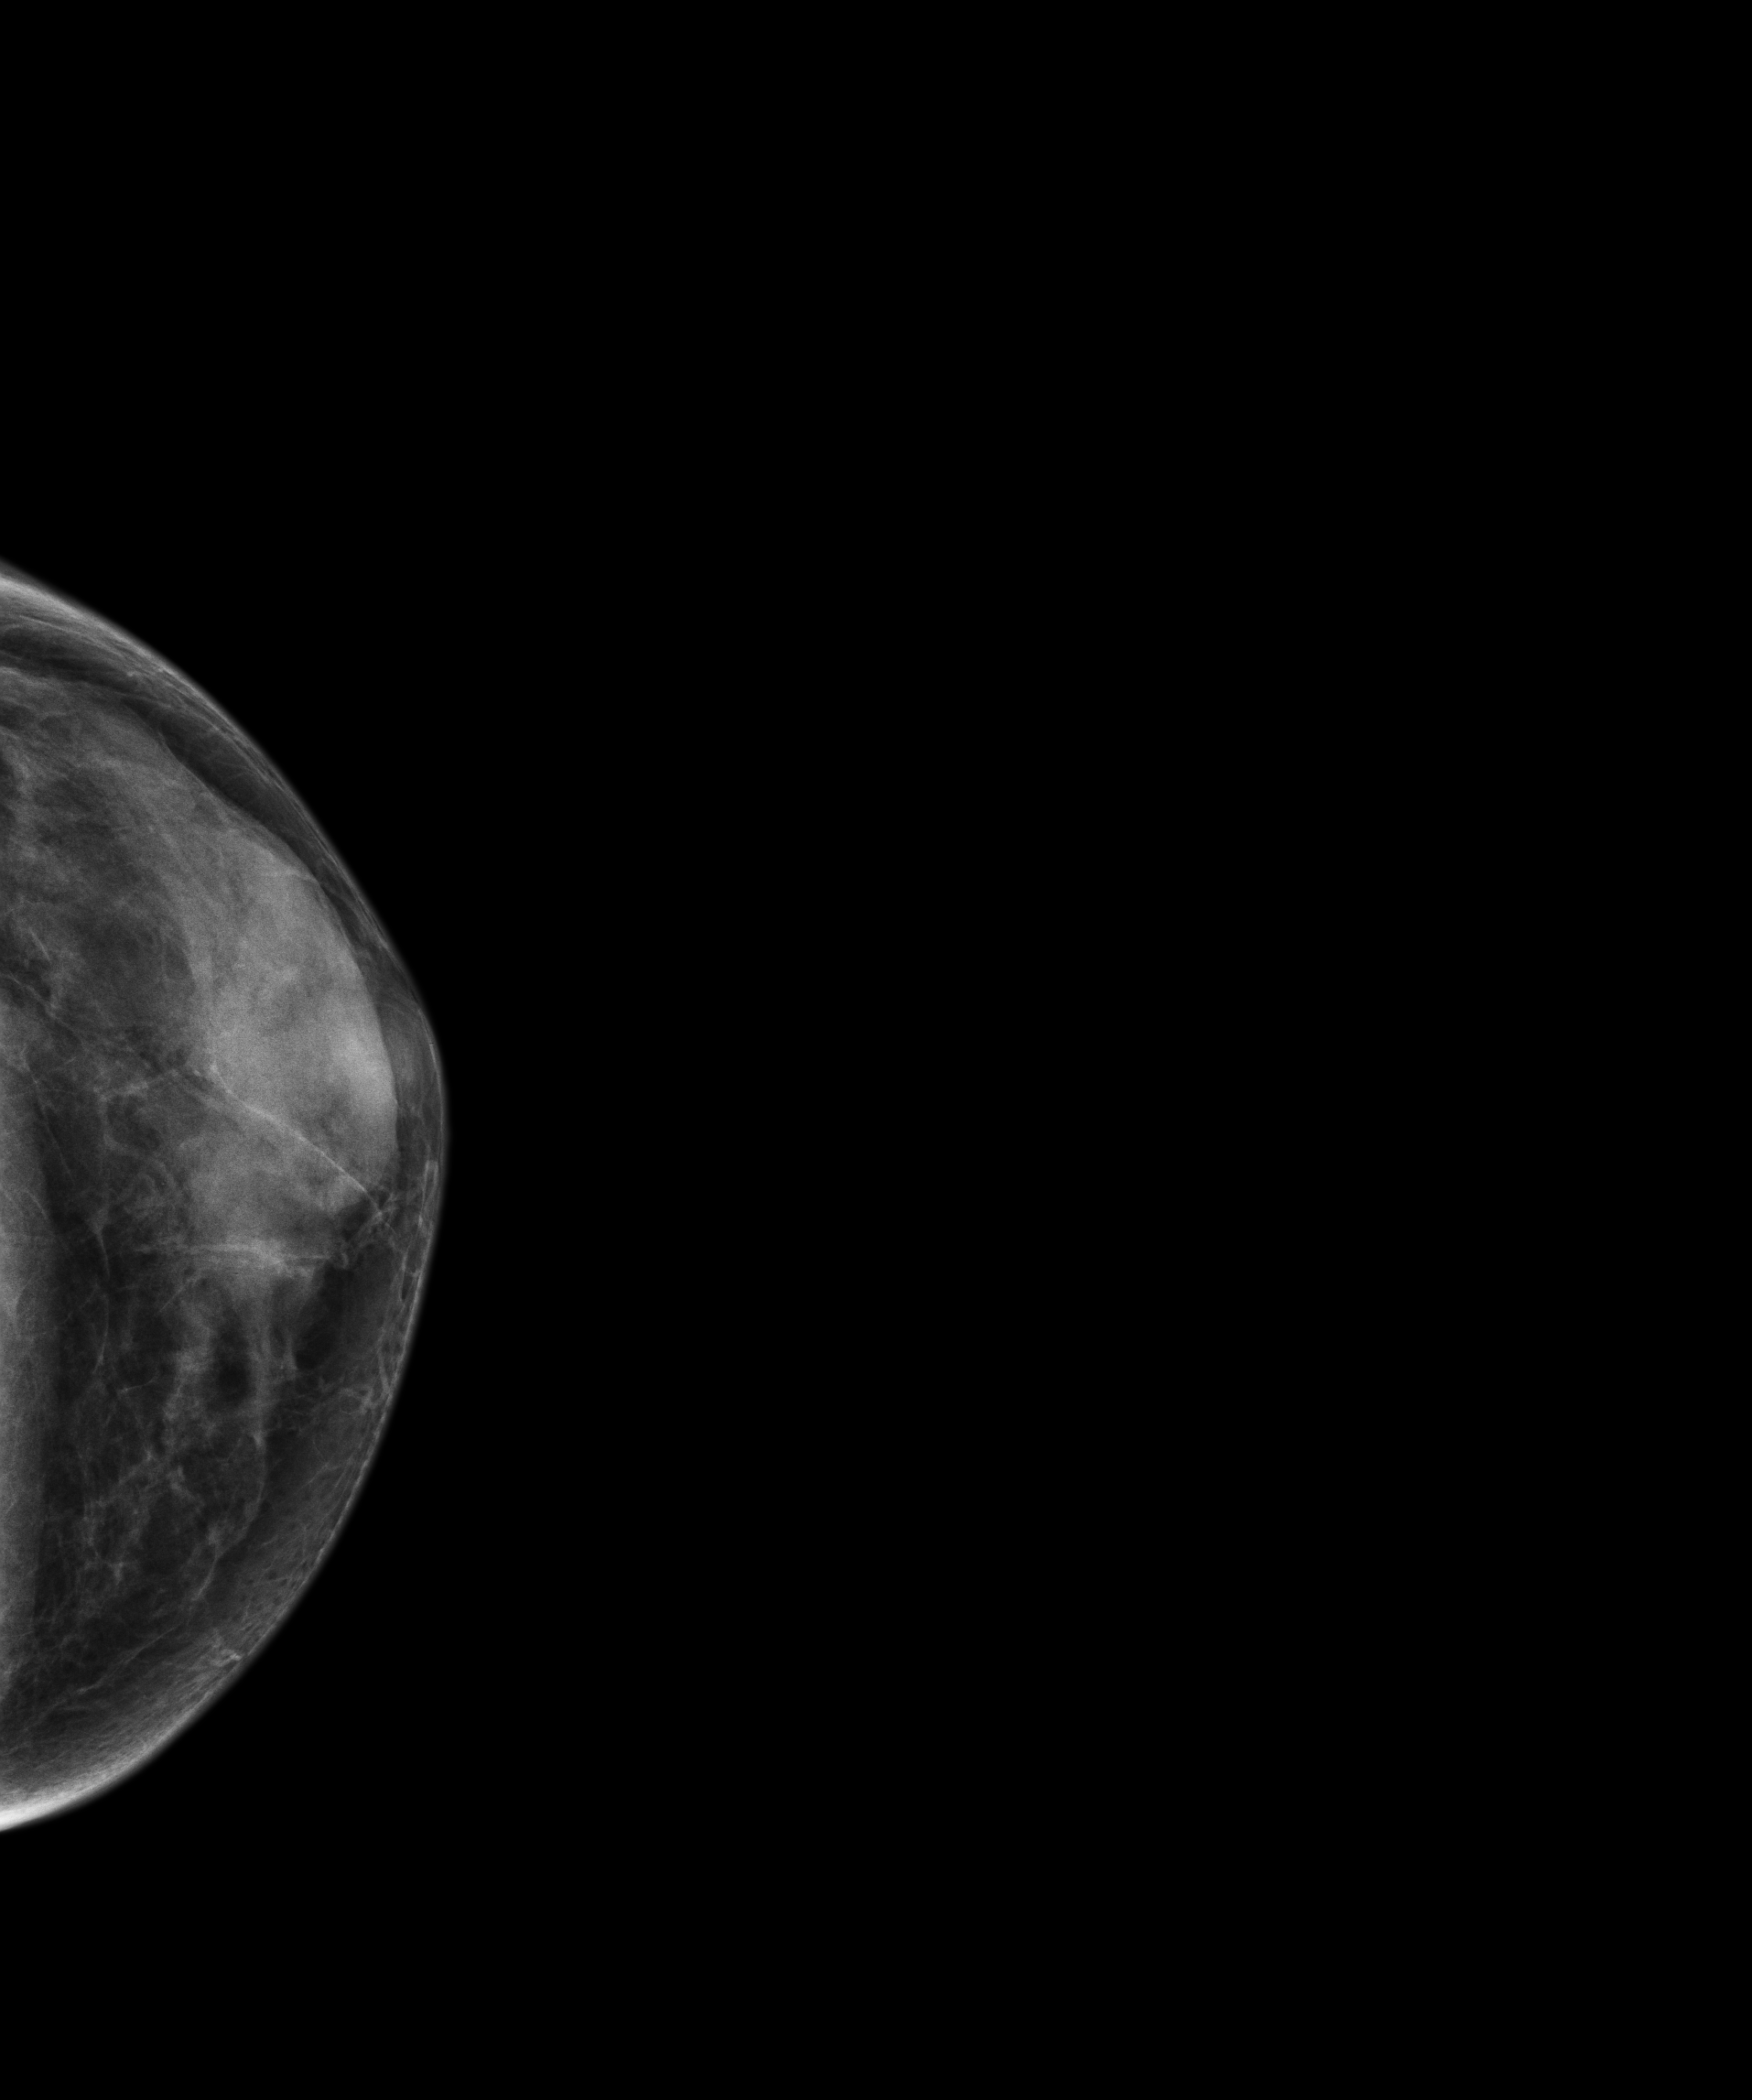
Full-field digital mammogram (FFDM); left breast; CC view; screening examination; compressed breast thickness 23 mm; system: Senographe Essential ADS_56.21.3. Female patient, age 55 years.
Breast density at the screening exam (both breasts): extremely dense (BI-RADS density category d). Final BI-RADS assessment for this screening round (tomosynthesis exam, both breasts): category 1. Recall: no recall after this screen.